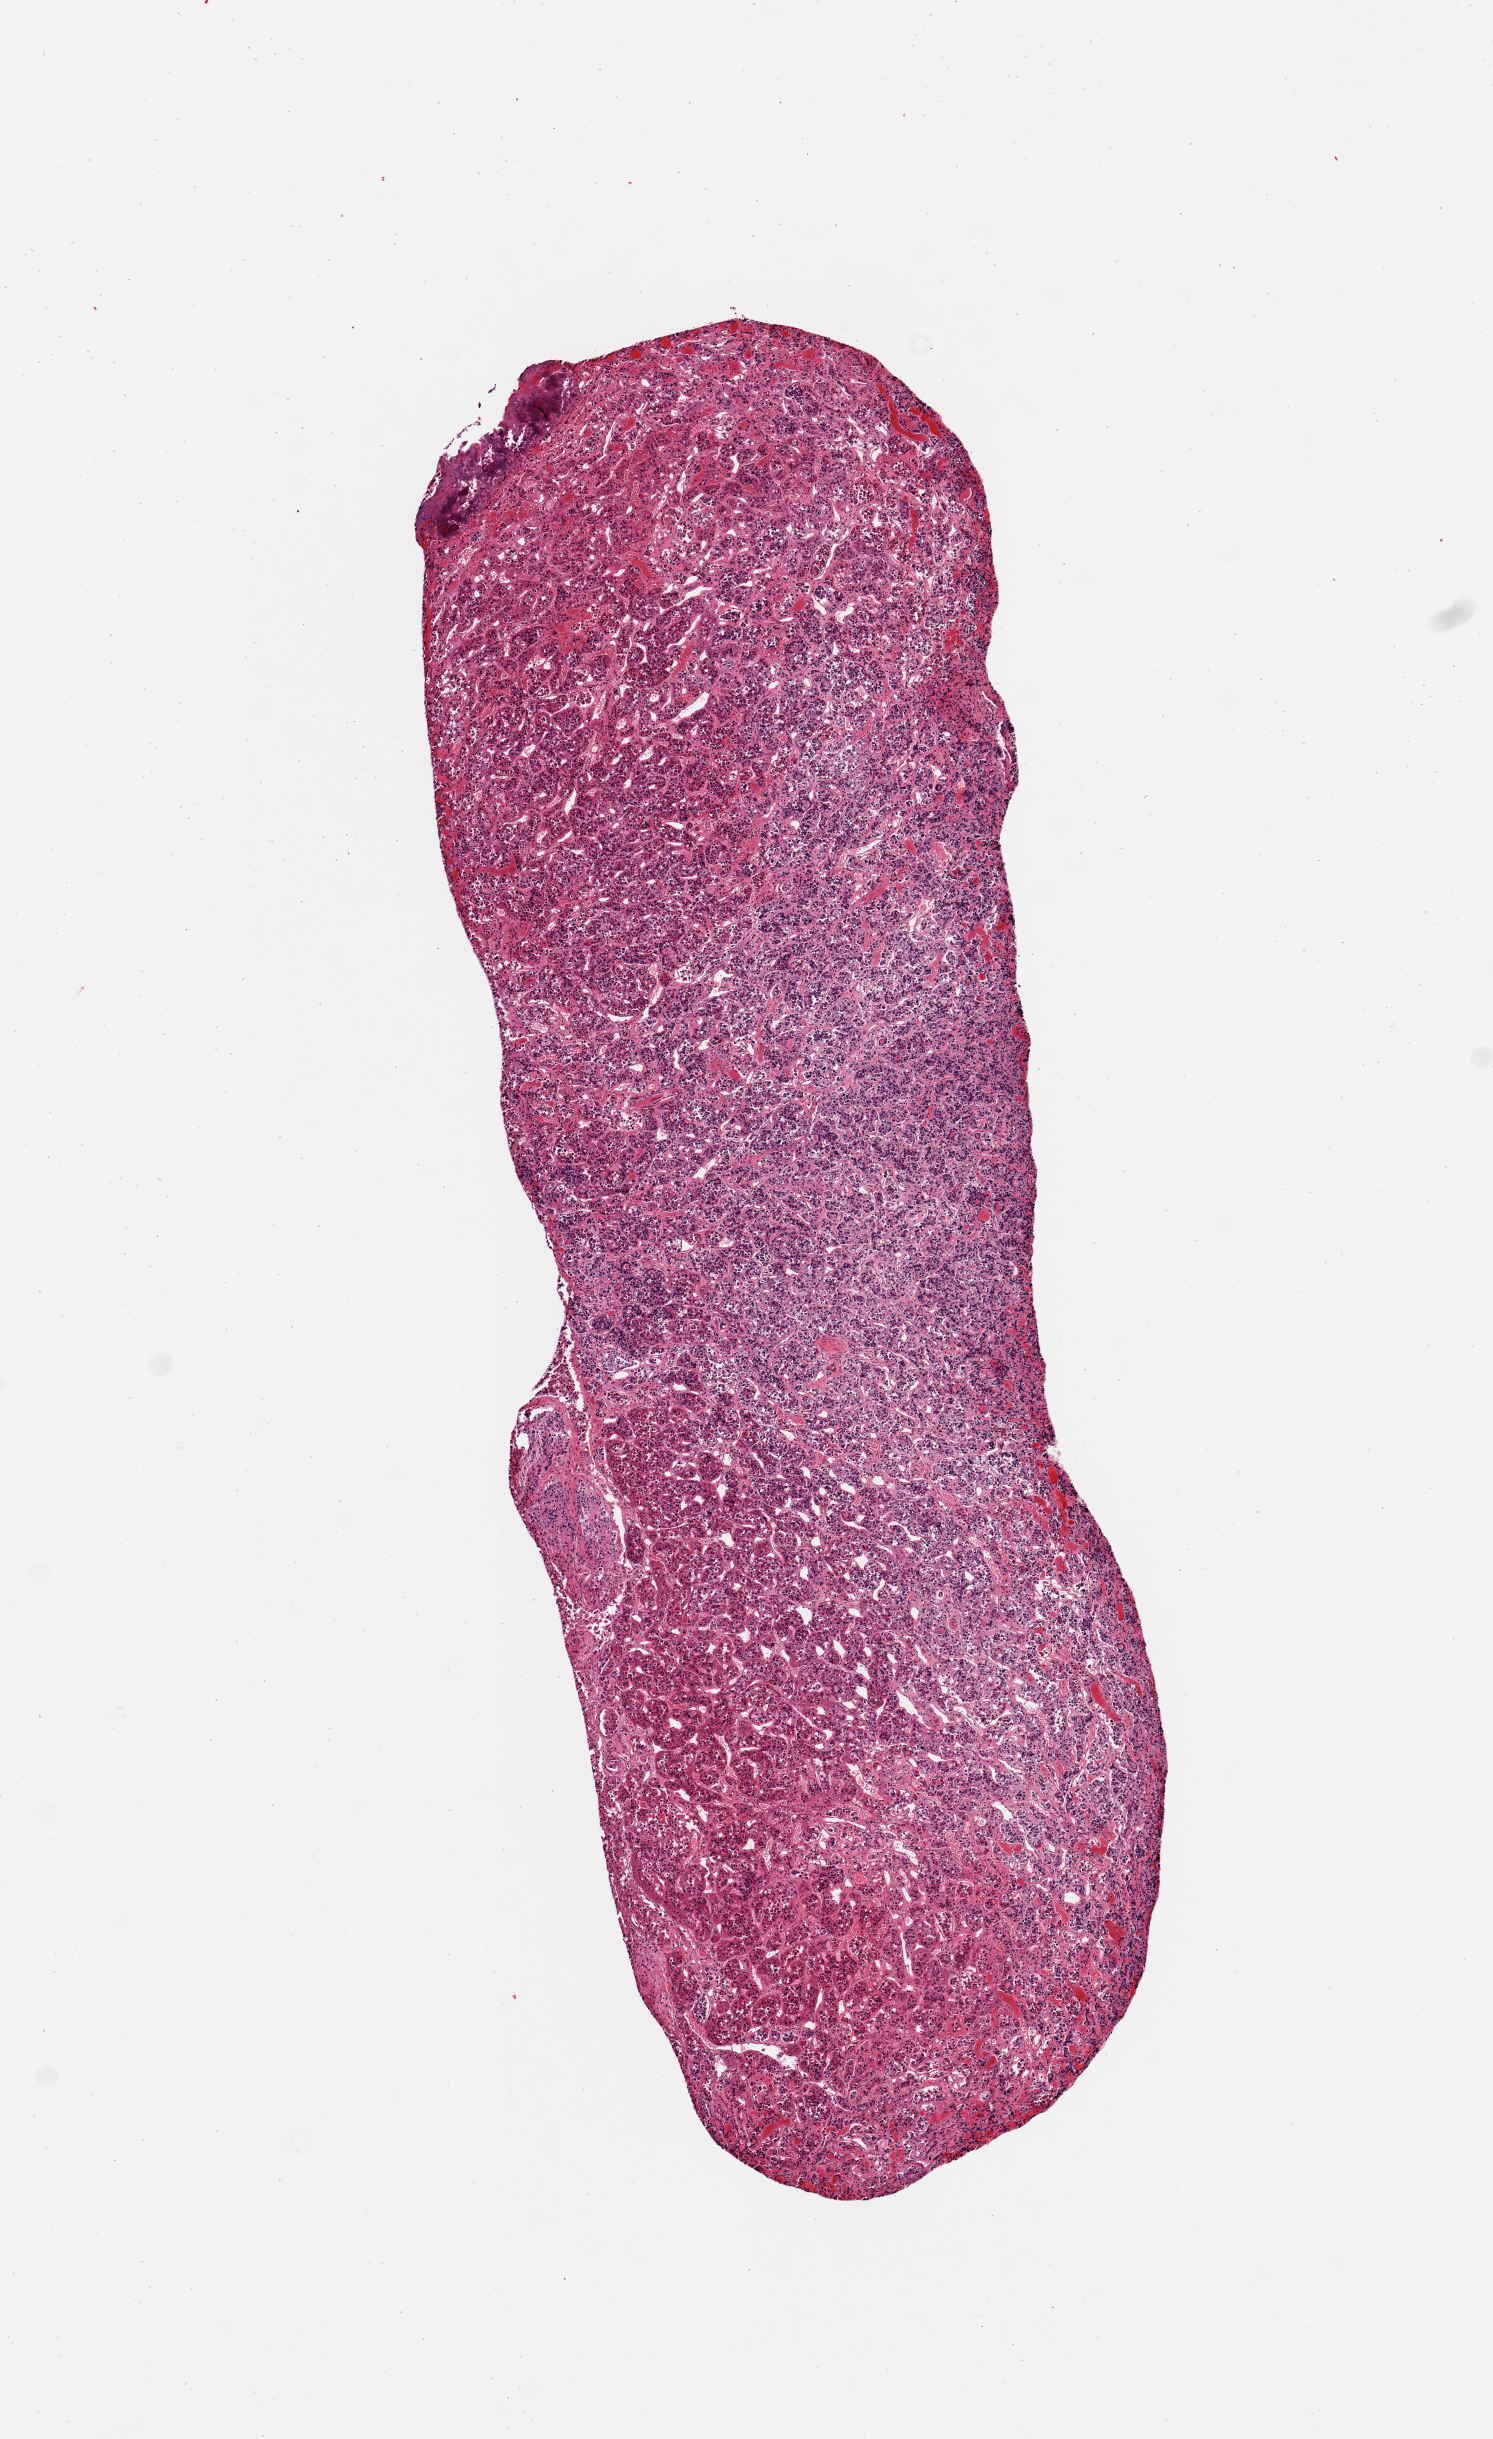
Whole-slide image, H&E stain, brightfield — shown as a low-resolution overview of the whole scanned area (about 5.9 x 9.6 mm), PAXgene-fixed paraffin-embedded (PFPE) section, section of pituitary (target tissue), tissue donor sample. Male donor.
Pathologist's review note for this sample: 1 piece; adenohypophysis.